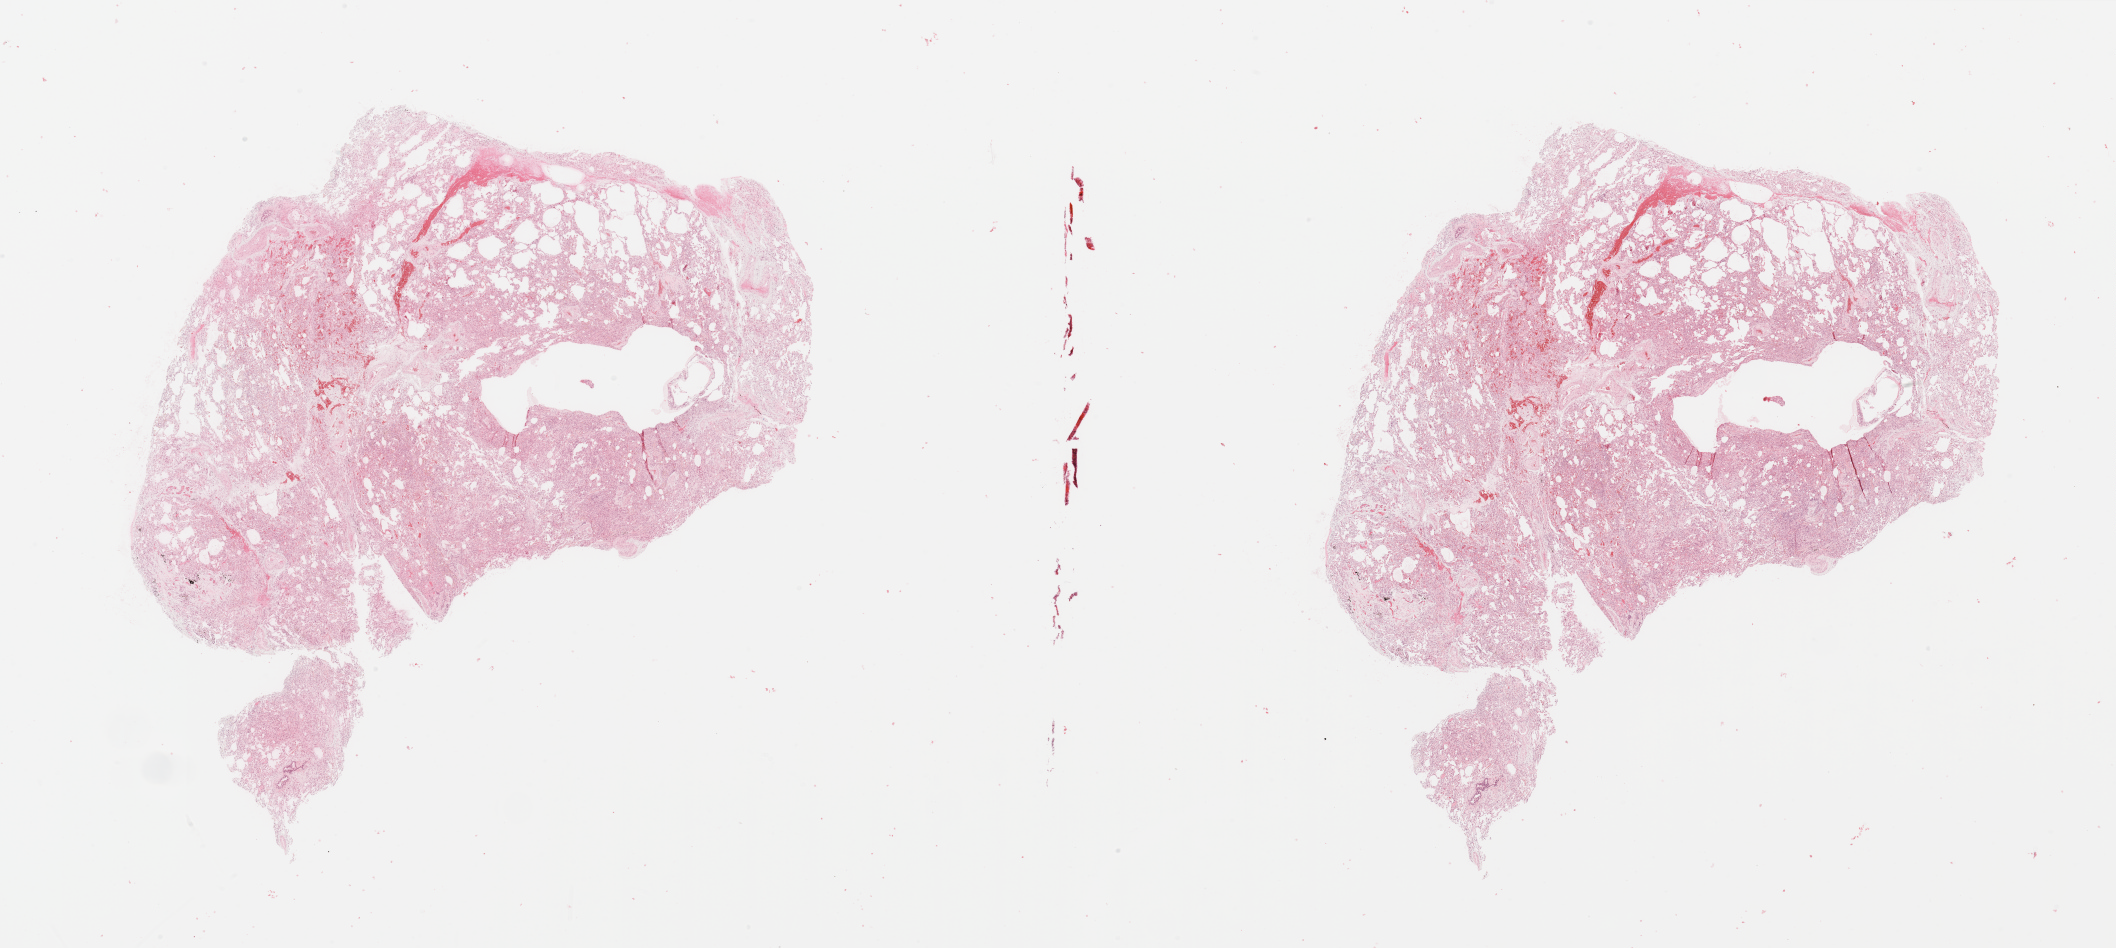
H&E whole-slide image, a low-resolution overview of the entire scanned area, about 33.5 x 15.0 mm, normal (non-tumour) tissue sample, sampled site: lung. Female, 66 y/o.
This section: normal (non-tumour) tissue from the same patient. Patient diagnosis: Squamous cell carcinoma, NOS.